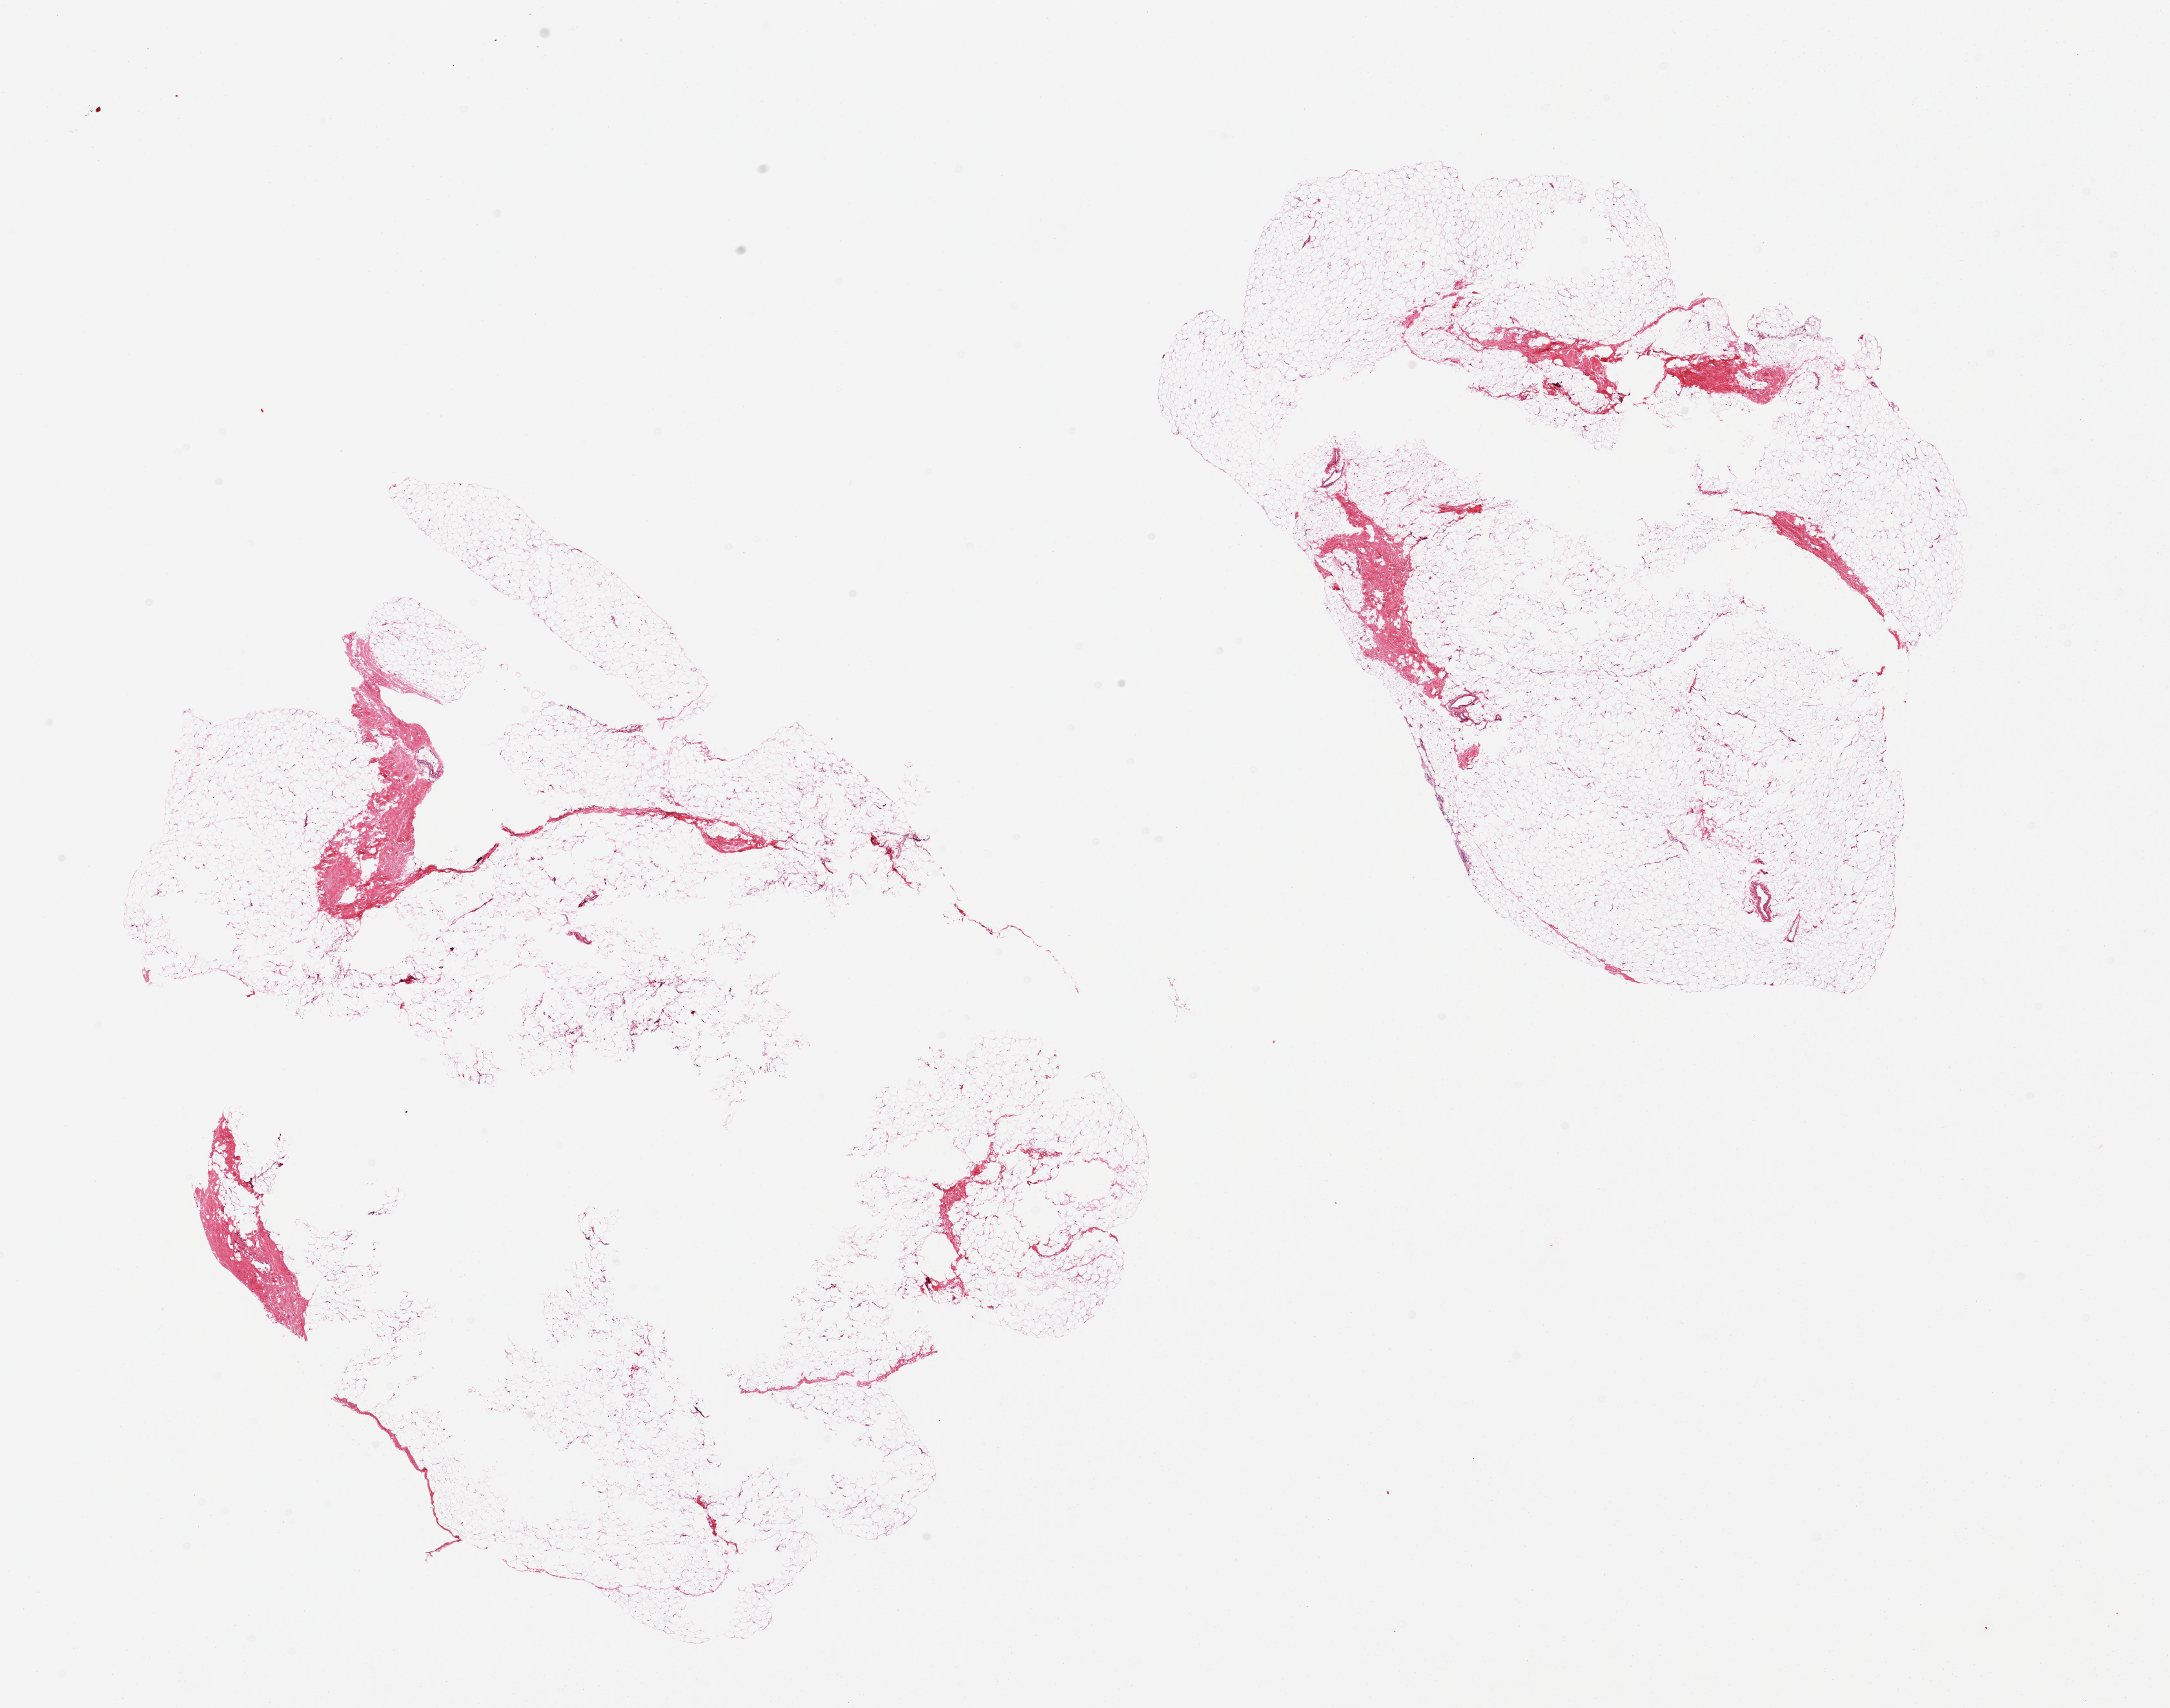
Digitized H&E-stained section, low-resolution overview of the scanned area, about 26.6 x 20.9 mm (acquisition: 20x scan); PAXgene-fixed paraffin-embedded (PFPE) section; sampled site (target tissue): breast; tissue donor sample.
• reviewer comment on this tissue sample: 2 pieces, large central defects (?poor fixation), small representation of fibrous tissue, no ductal elements